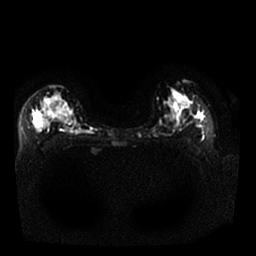
Breast MRI, one axial slice. Slice 15 of 25 in the series (ordered by position). Diffusion-weighted series; image 2 of 4 stored at this slice position (different b-values; order by instance number). 1.5 T. 4 mm slice thickness. 256 × 256 image matrix, field of view 340 × 340 mm. Female patient.
Annotated regions visible in this slice (manually delineated by an expert):
- tumour on diffusion-weighted imaging: bounding box [x1, y1, x2, y2] px = [39, 105, 64, 126]